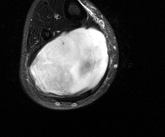
MRI of an extremity soft-tissue mass, one axial slice; slice 53 of 81 in the series (ordered by position); T2-weighted fat-saturated; MR volume resampled by the dataset authors to the PET/CT grid (not the native acquisition matrix); 165 × 137 image matrix. Male patient. Case-level facts recorded for this patient, not image findings: histological type: liposarcoma - round cell; grade: high; site of the primary tumour: right calf.
Annotated regions visible in this slice (expert contour drawn on MRI and transferred to this co-registered scan by the dataset authors):
- gross tumour volume (mass): bounding box <30,27,109,97> (left, top, right, bottom; pixels)